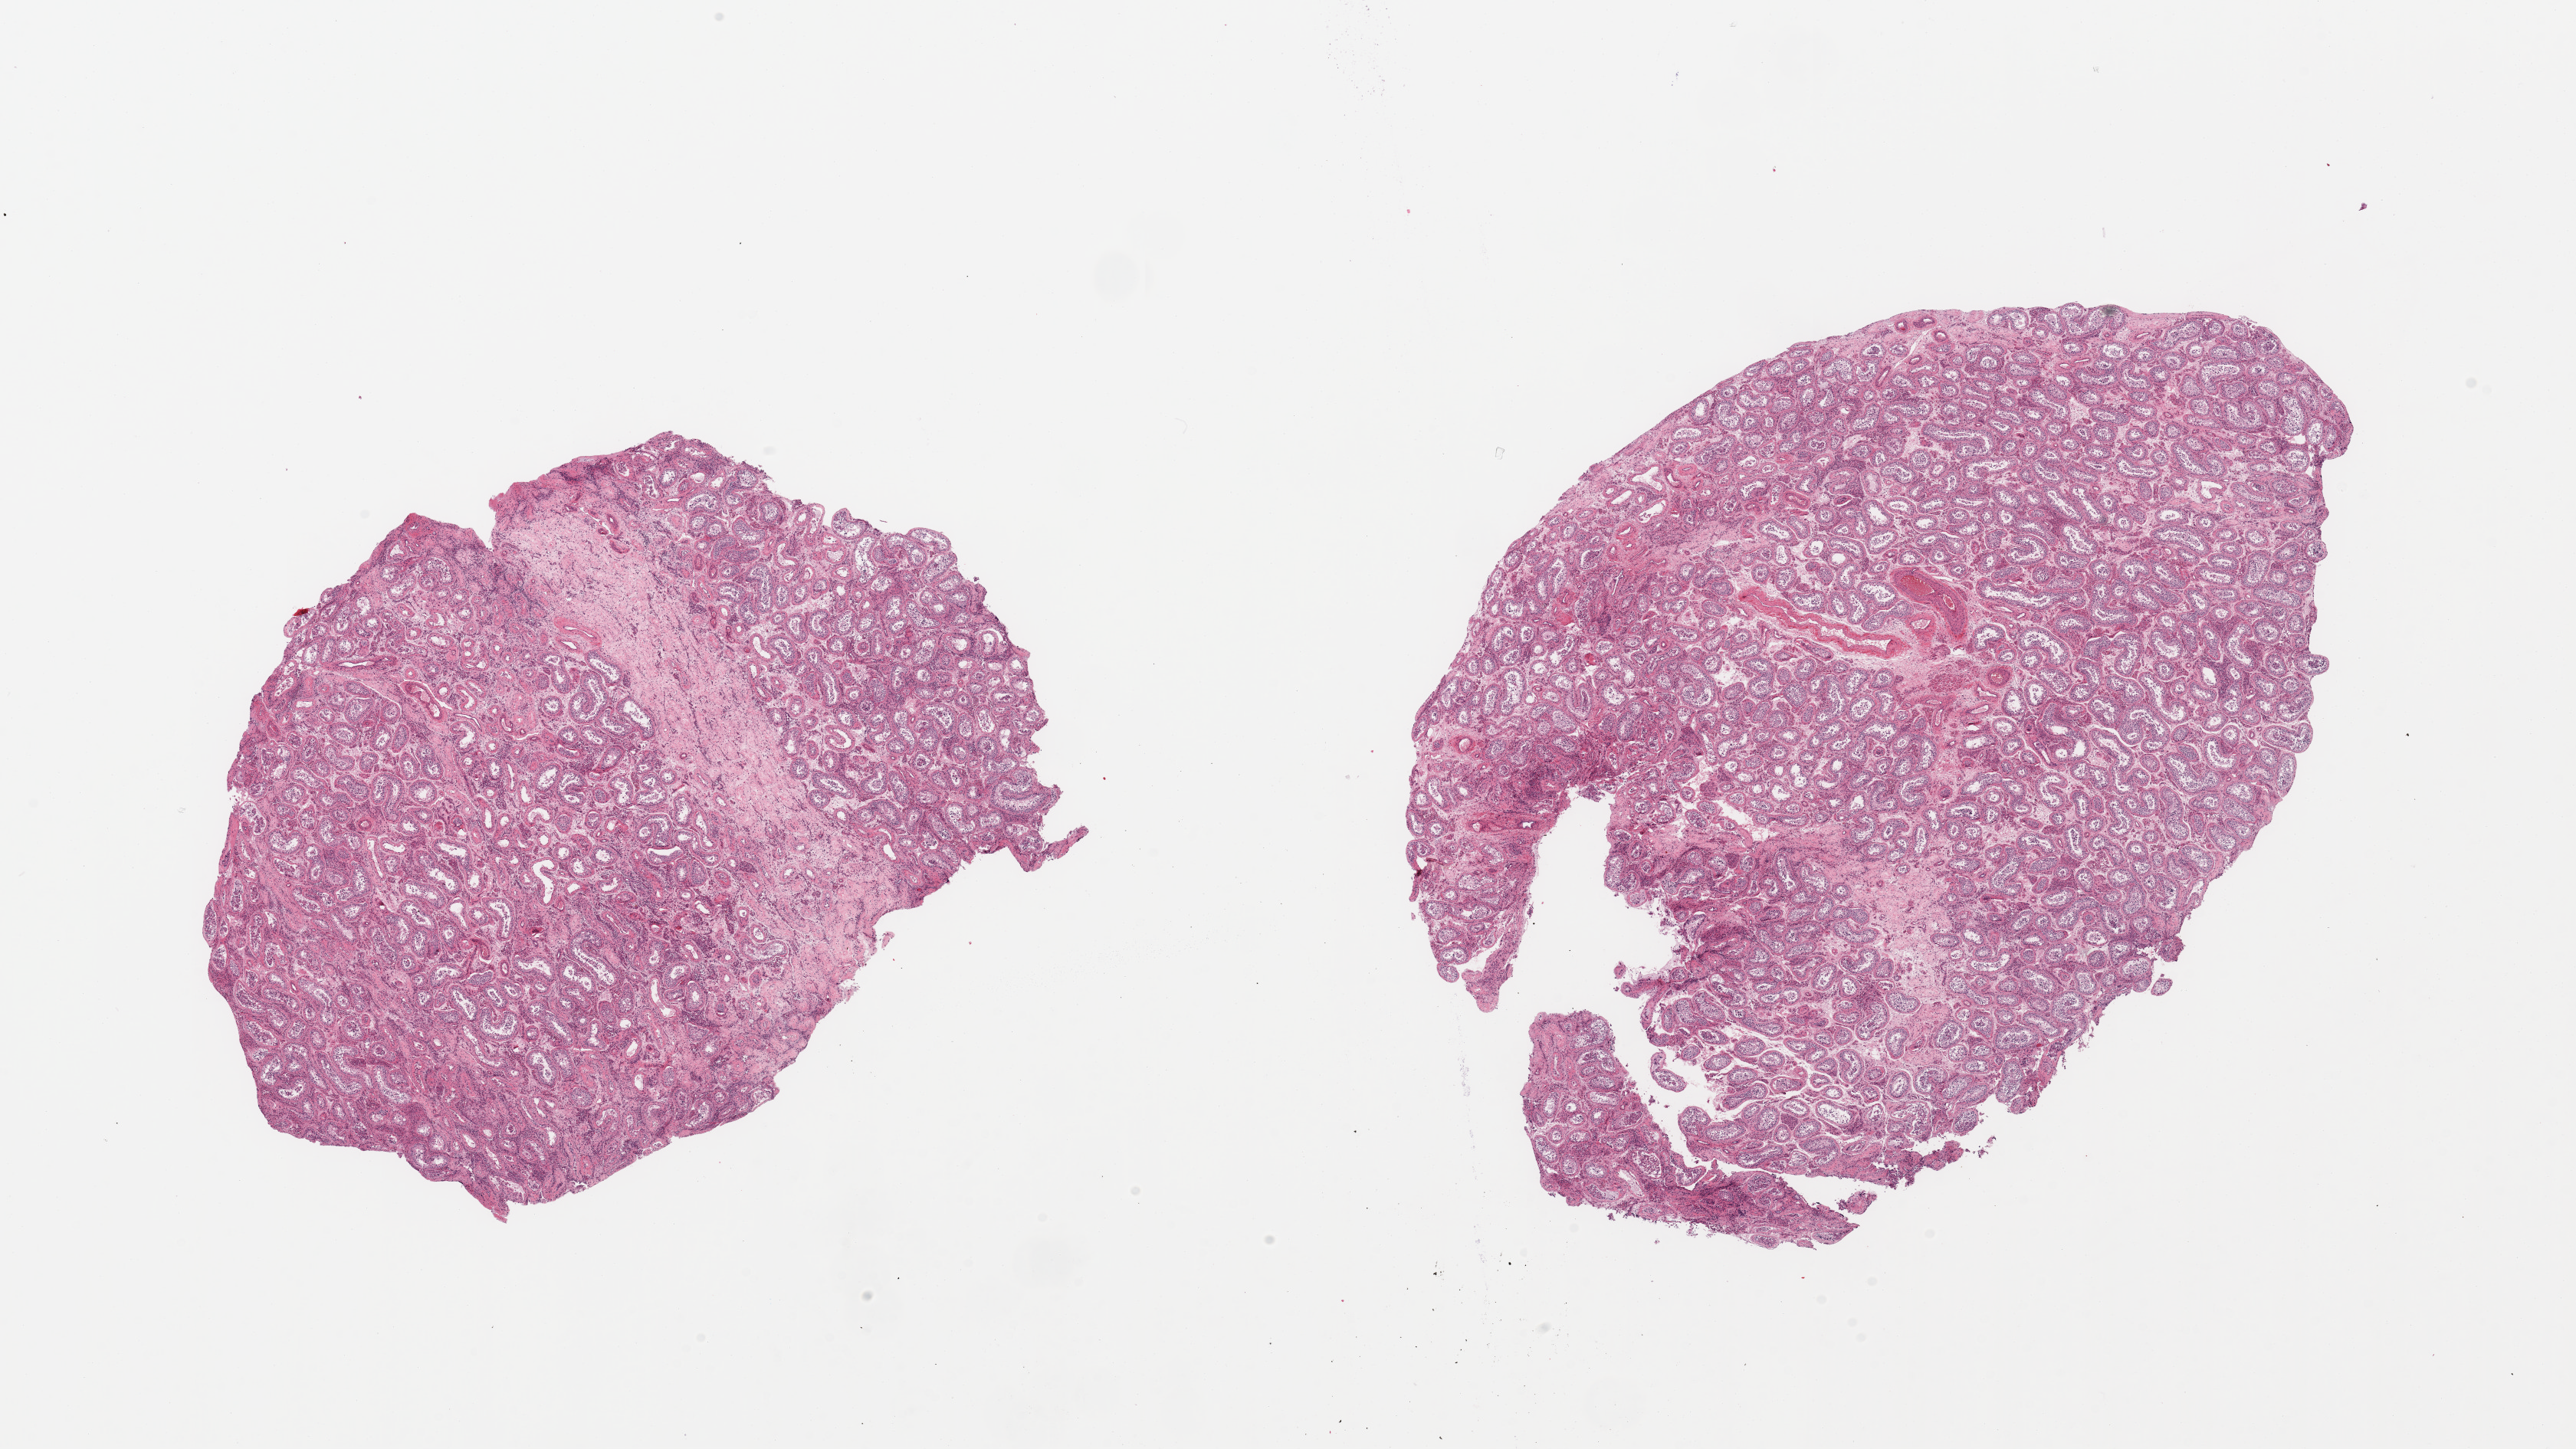
Whole-slide image, haematoxylin and eosin stain, whole scanned area (about 26.6 x 15.0 mm, slide scanned at 20x) shown as a low-resolution overview. PAXgene-fixed paraffin-embedded (PFPE) section. Target tissue: testis. Donor tissue sample. Donor: male.
Review note (as recorded): 2 pieces; active spermatogenesis.